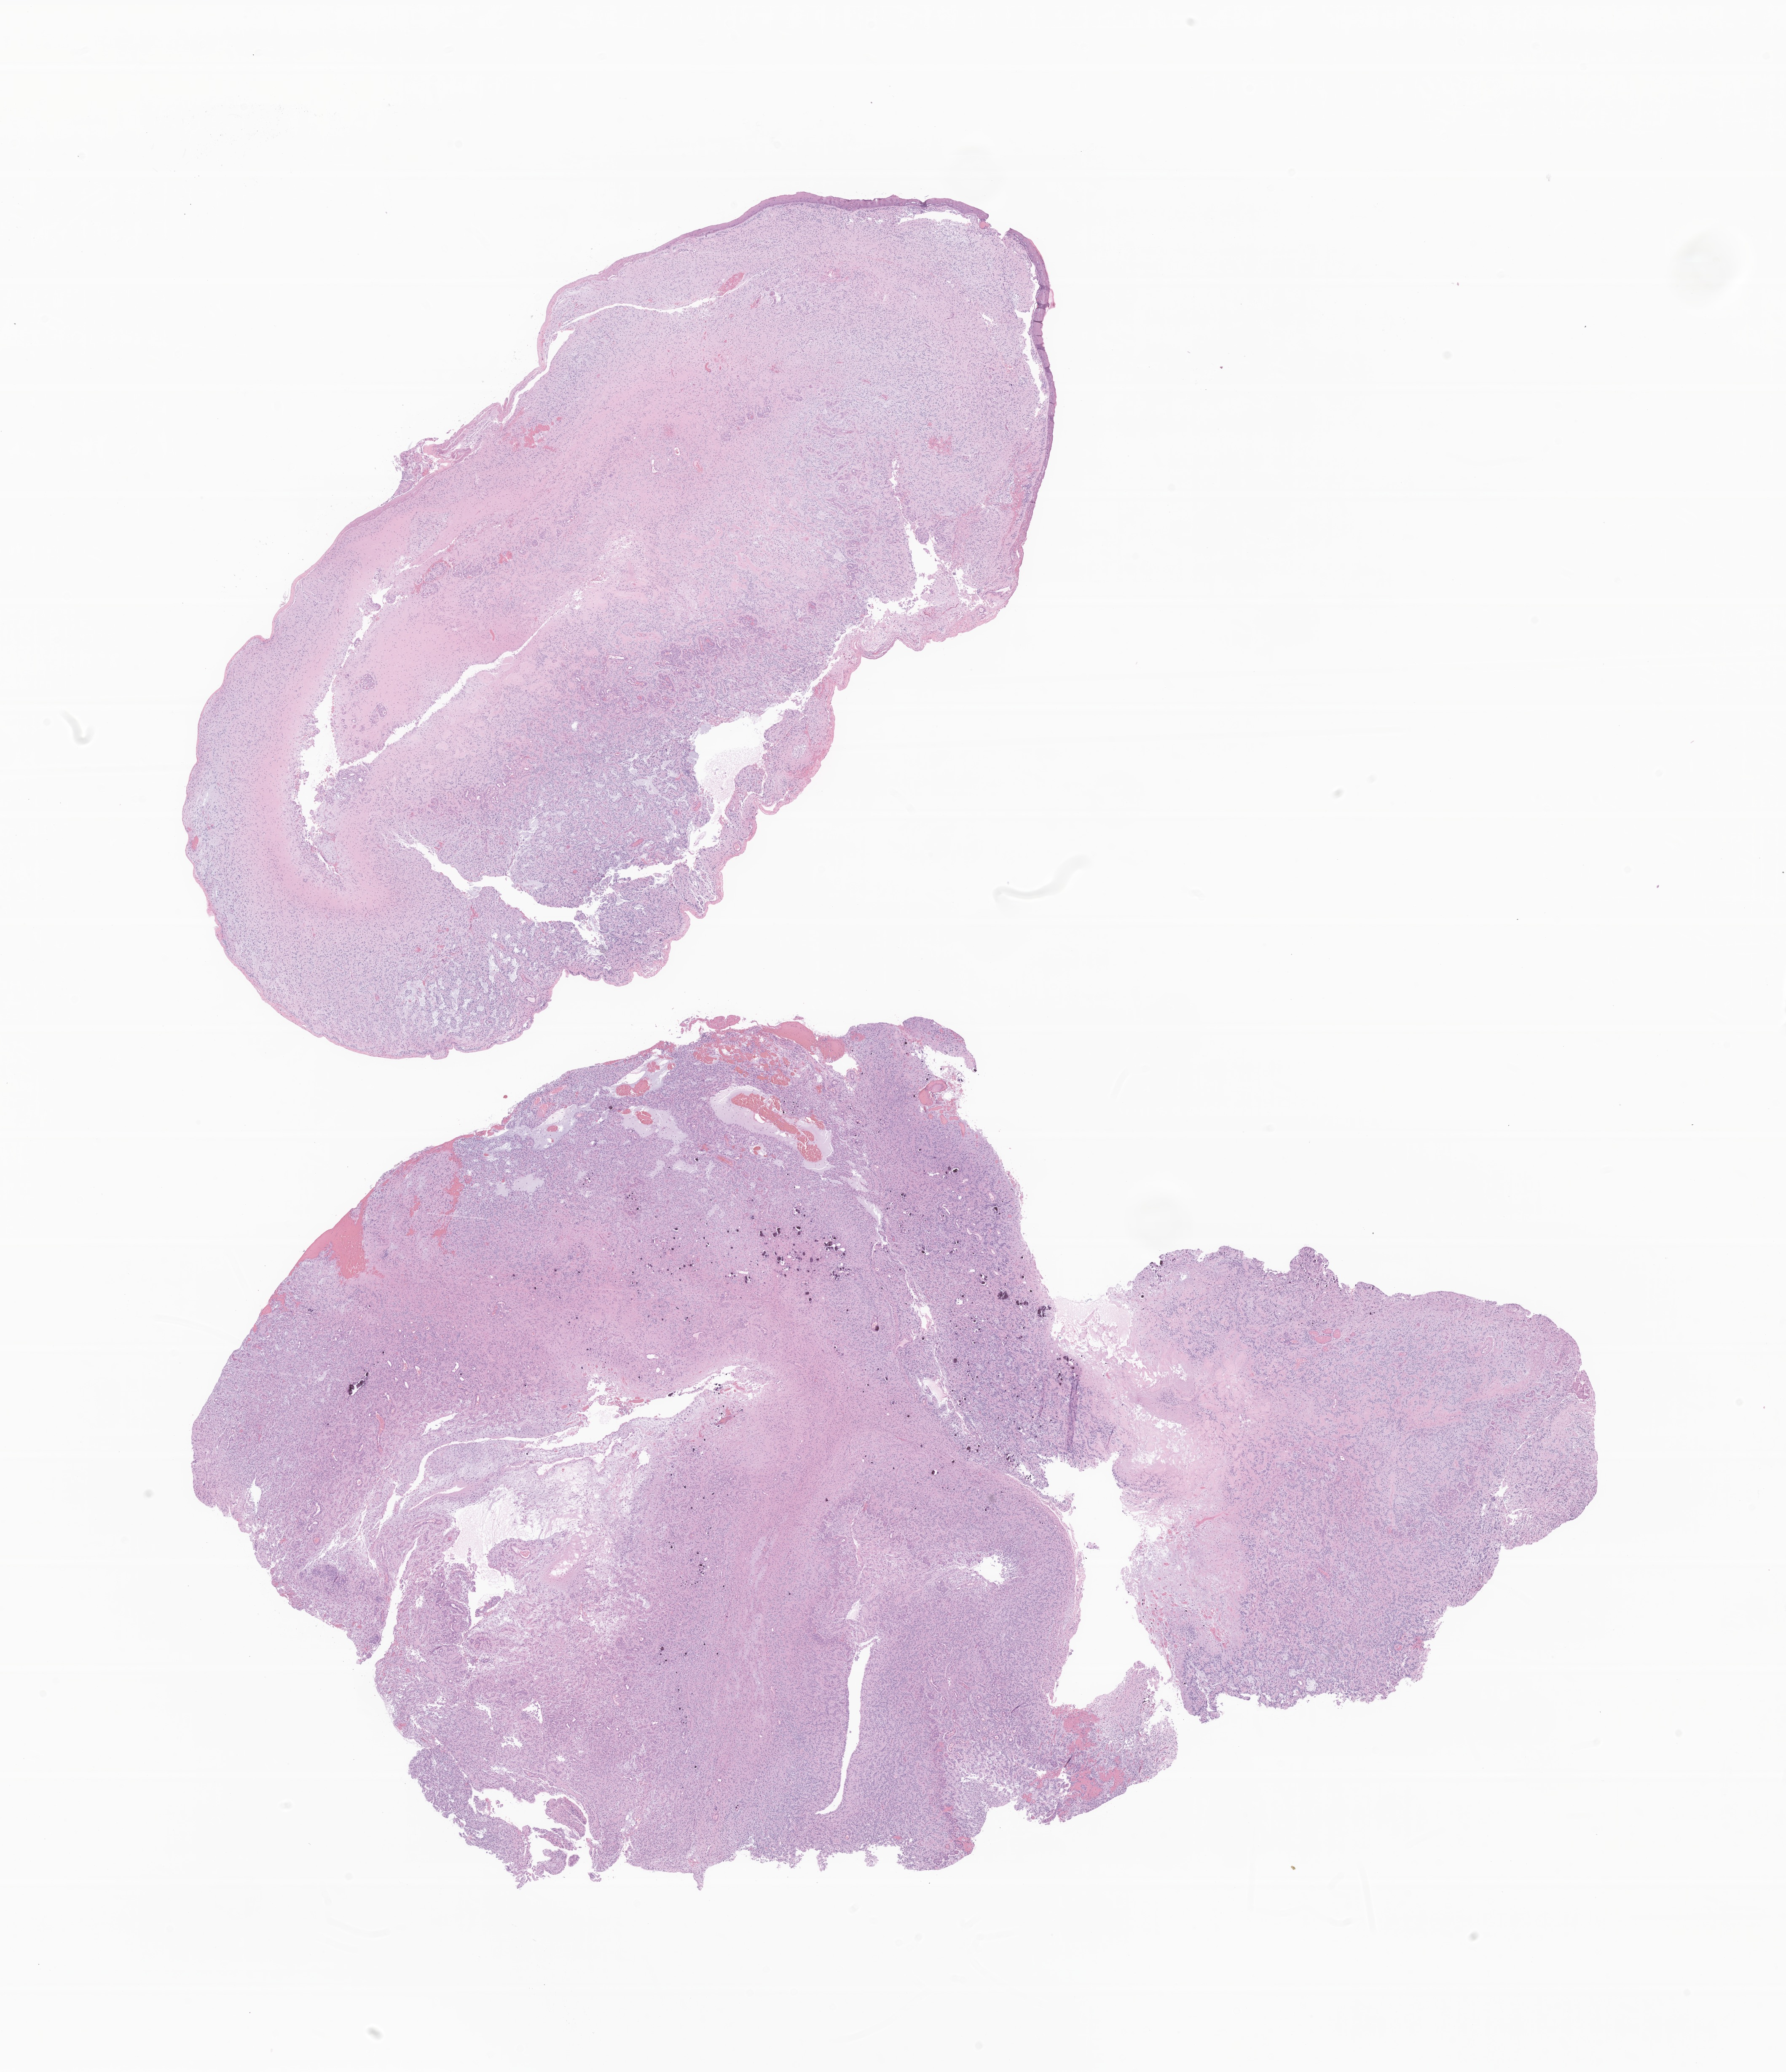
H&E whole-slide image of tumor tissue from the cerebellum — a low-resolution overview of the entire scanned area, about 17.9 x 20.7 mm; FFPE section. Patient: male, age 138 months (11 years 6 months).
- recorded diagnosis: Pilocytic astrocytoma